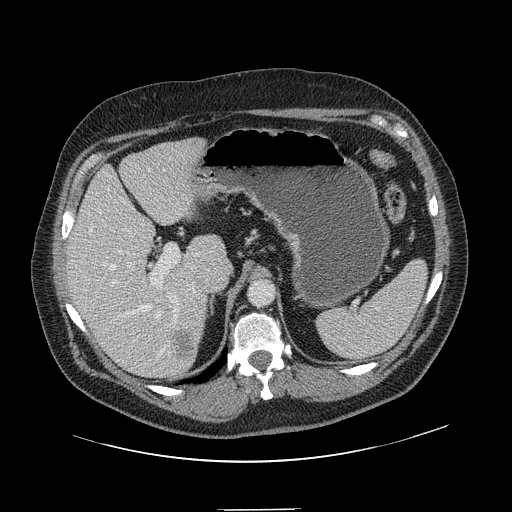
Contrast-enhanced abdominal CT, one axial slice. 120 kVp. Intravenous contrast given. Soft-tissue window (W 400 / L 40 HU). 2.5 mm slice thickness. 512 × 512 image matrix, field of view 451 × 451 mm. Male patient, age 61 years. Case-level facts recorded for this patient, not image findings: diagnosis: colorectal cancer liver metastases, imaged before liver resection; multiple liver metastases: yes; largest metastasis: 2.6 cm; disease in both lobes: yes.
Outlined on this slice (expert manual segmentation):
- hepatic veins: bounding box [x1, y1, x2, y2] px = [88, 210, 180, 355]
- liver: [68, 139, 225, 378]
- planned liver remnant (the part of the liver to remain after resection): [68, 146, 225, 364]
- portal vein (with intrahepatic branches): [107, 186, 187, 303]
- liver metastasis: [175, 334, 196, 362]